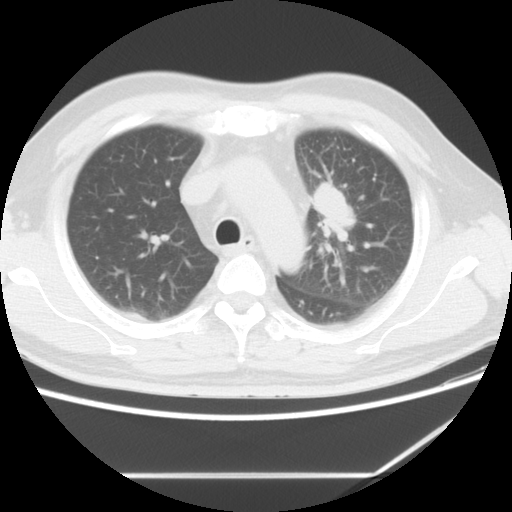
Chest CT, one axial slice. Reconstruction kernel STANDARD. Lung window (W 1500 / L -600 HU). 5 mm slice thickness. 512 × 512 image matrix, field of view 350 × 350 mm. Patient: male, 56 years. From the clinical record (not read from this slice): clinical TNM (as recorded): T2 N3 M1.
Outlined on this slice (rectangle marked by the reading radiologist):
- lung tumour (recorded histology: adenocarcinoma): box from (x=309, y=179) to (x=353, y=242) px